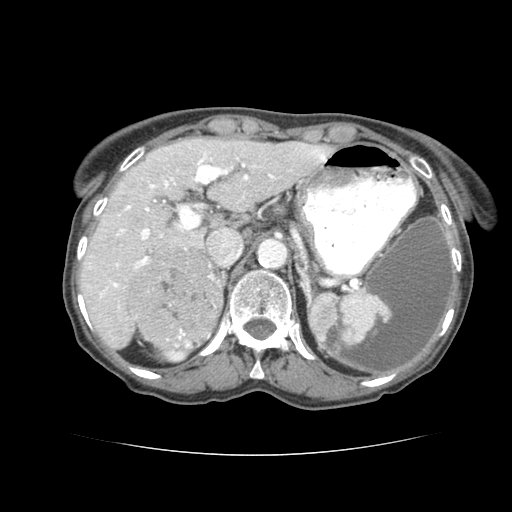
Contrast-enhanced abdominal CT (liver protocol), one axial slice; position 50 of 77 along the scan axis; reconstruction kernel STANDARD; 120 kVp; soft-tissue window (W 400 / L 40 HU); 2.5 mm slice thickness; 512 × 512 image matrix, field of view 340 × 340 mm. Case-level facts recorded for this patient, not image findings: diagnosis: hepatocellular carcinoma (patient treated with transarterial chemoembolisation; whether this scan precedes or follows treatment is not stated here); TNM stage (as recorded): Stage-I; Child-Pugh class: A; tumour differentiation: well differentiated; tumour nodularity: uninodular.
Outlined on this slice (semi-automatically segmented with operator editing):
- liver parenchyma outside the tumour (the mass and vessels are separate outlines, so this box may not span the whole liver): box from (x=80, y=134) to (x=334, y=346) px
- mass: (x=129, y=244)–(x=222, y=351)
- liver vessels: (x=86, y=150)–(x=270, y=329)